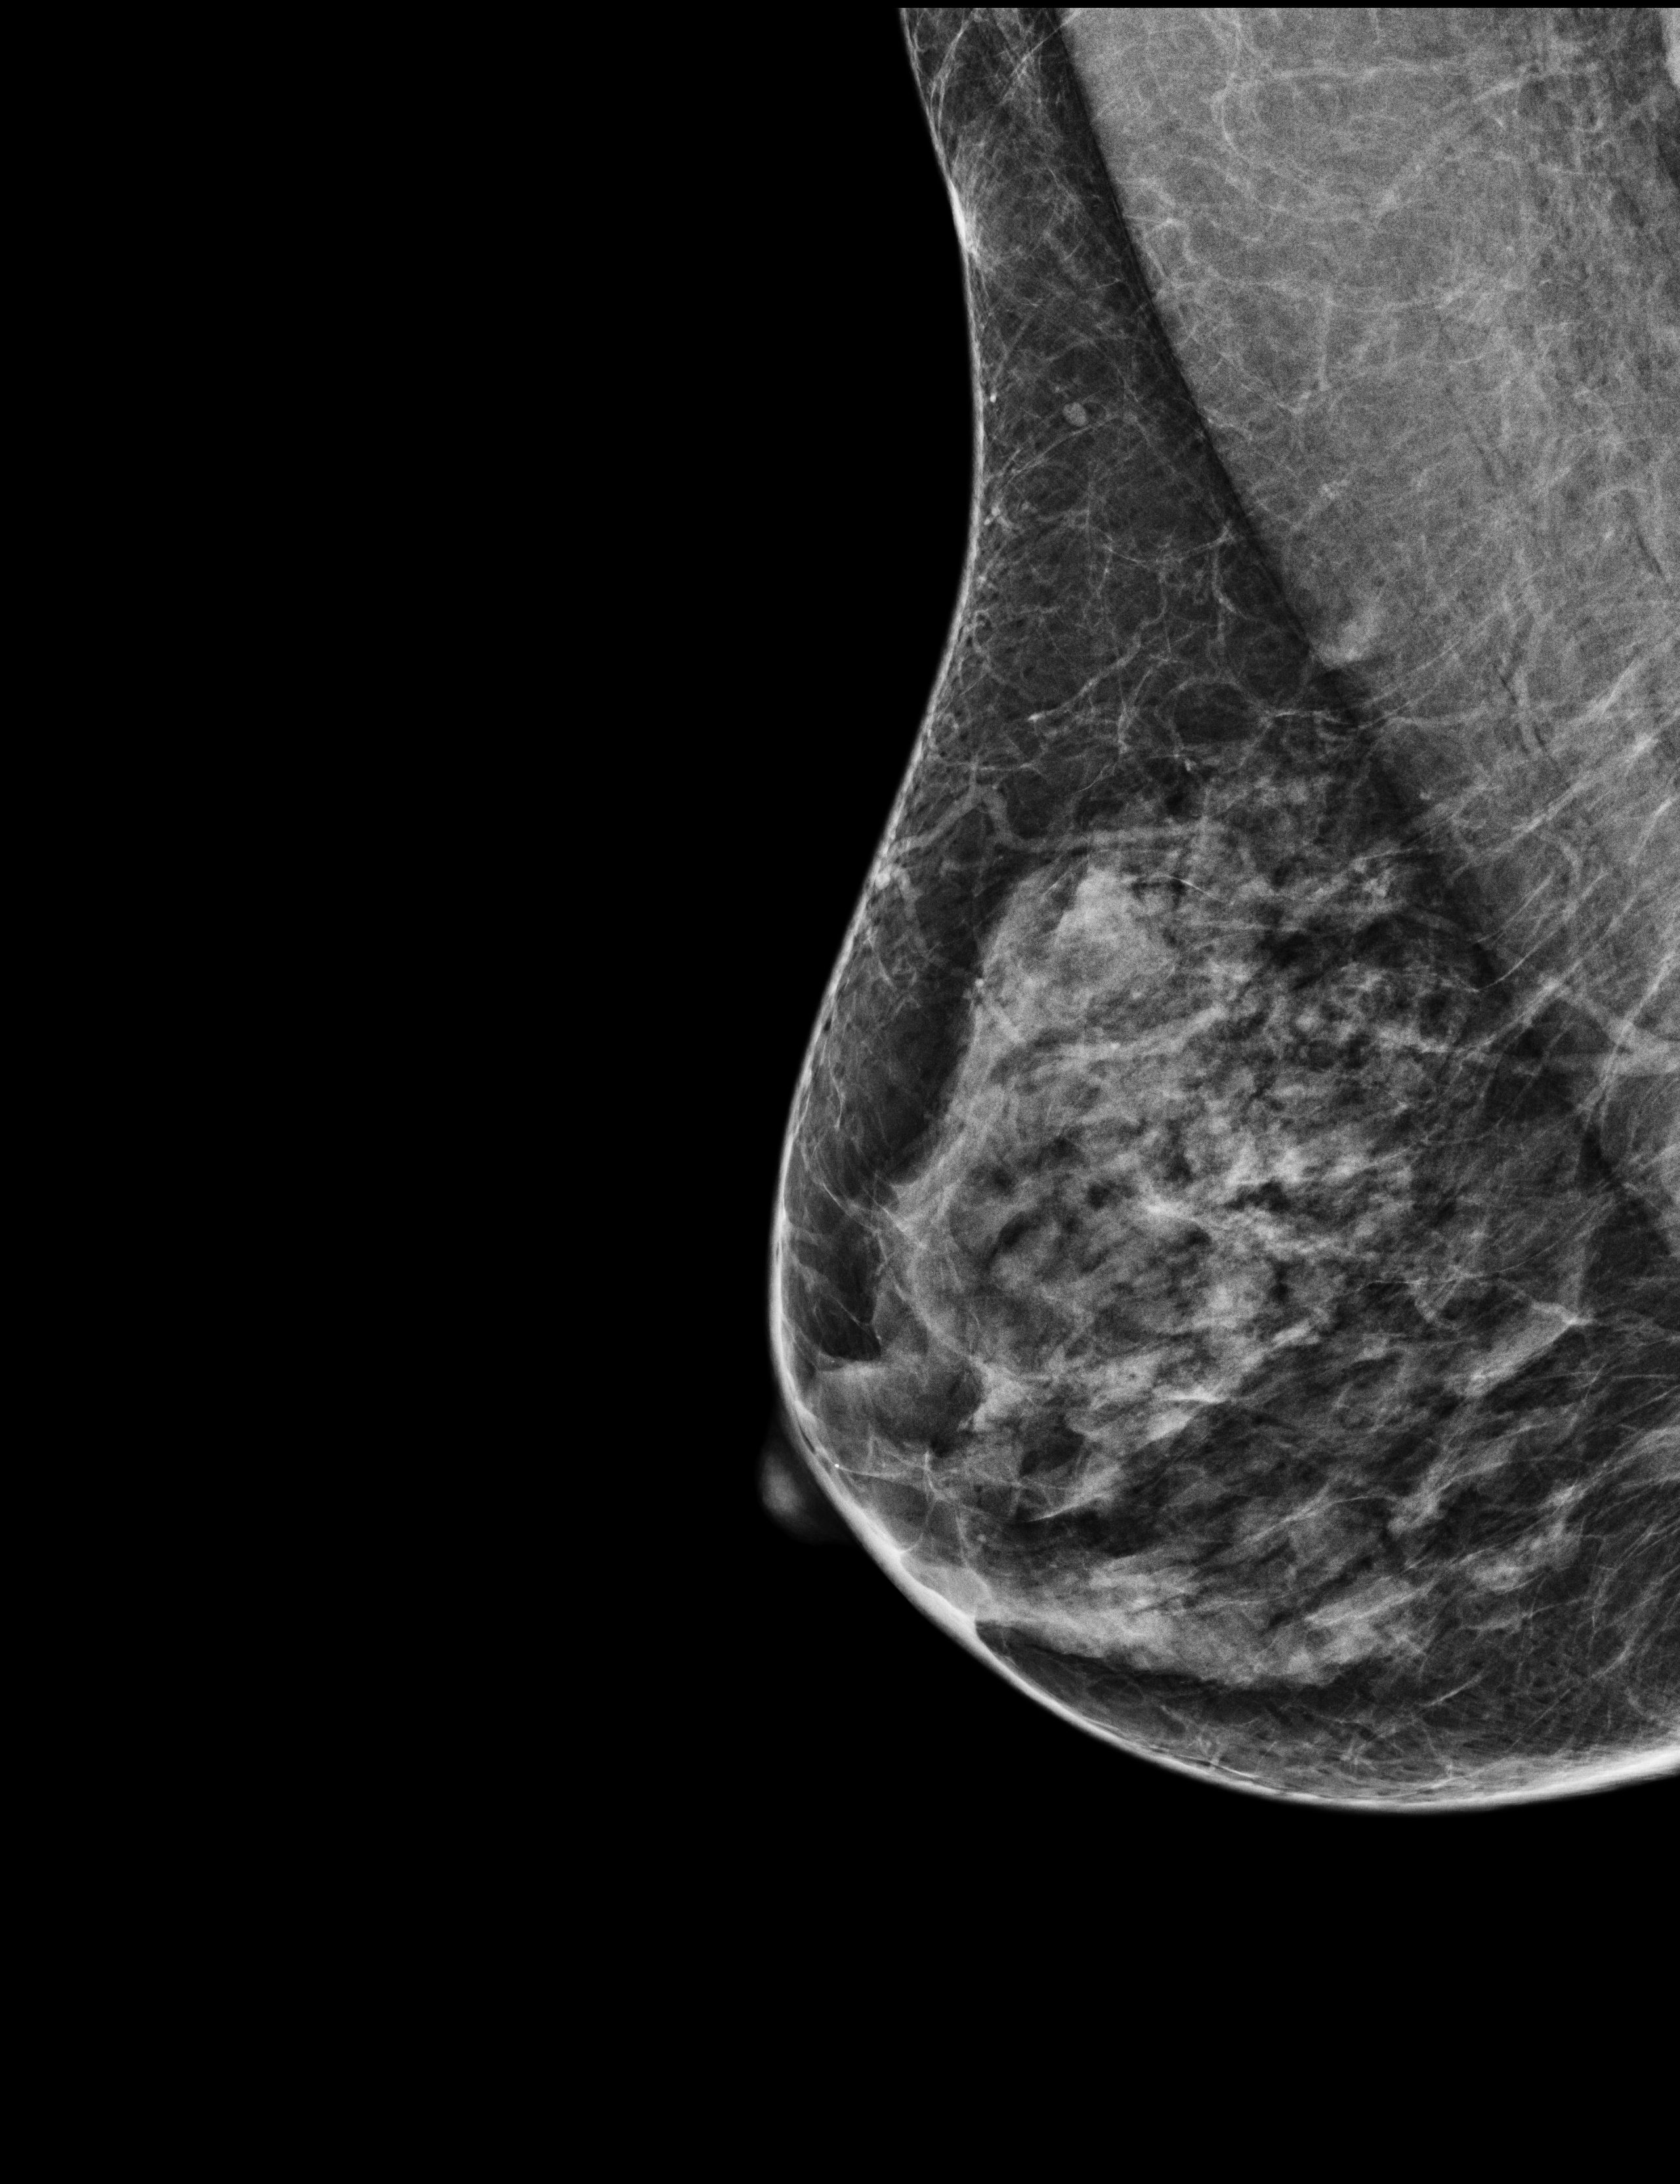
Annual screening mammography examination, compressed breast thickness 41 mm. Female patient, age 67 years.
Image type: full-field digital mammogram. Breast: right. Projection: medio-lateral oblique projection.